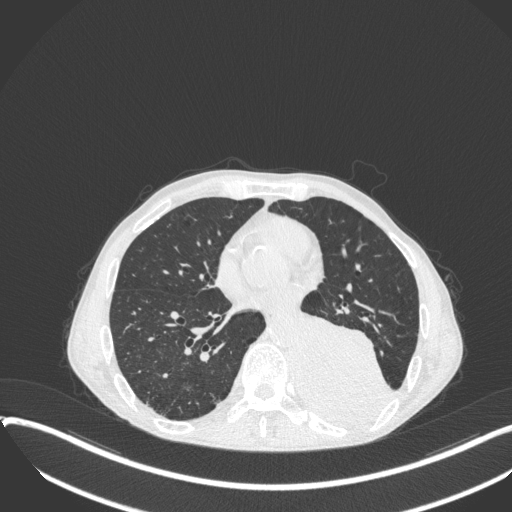
Chest CT, one axial slice; position 154 of 400 along the scan axis; reconstruction kernel B31f; 120 kVp; lung window (W 1500 / L -600 HU); 1 mm slice thickness; 512 × 512 image matrix. Male patient, age 57 years. Case-level facts recorded for this patient, not image findings: clinical TNM (as recorded): T4 N0 M0.
Structures marked on this image (rectangle marked by the reading radiologist):
- lung tumour (recorded histology: squamous cell carcinoma): bounding box (x1, y1, x2, y2) in pixels: (296, 307, 392, 432)